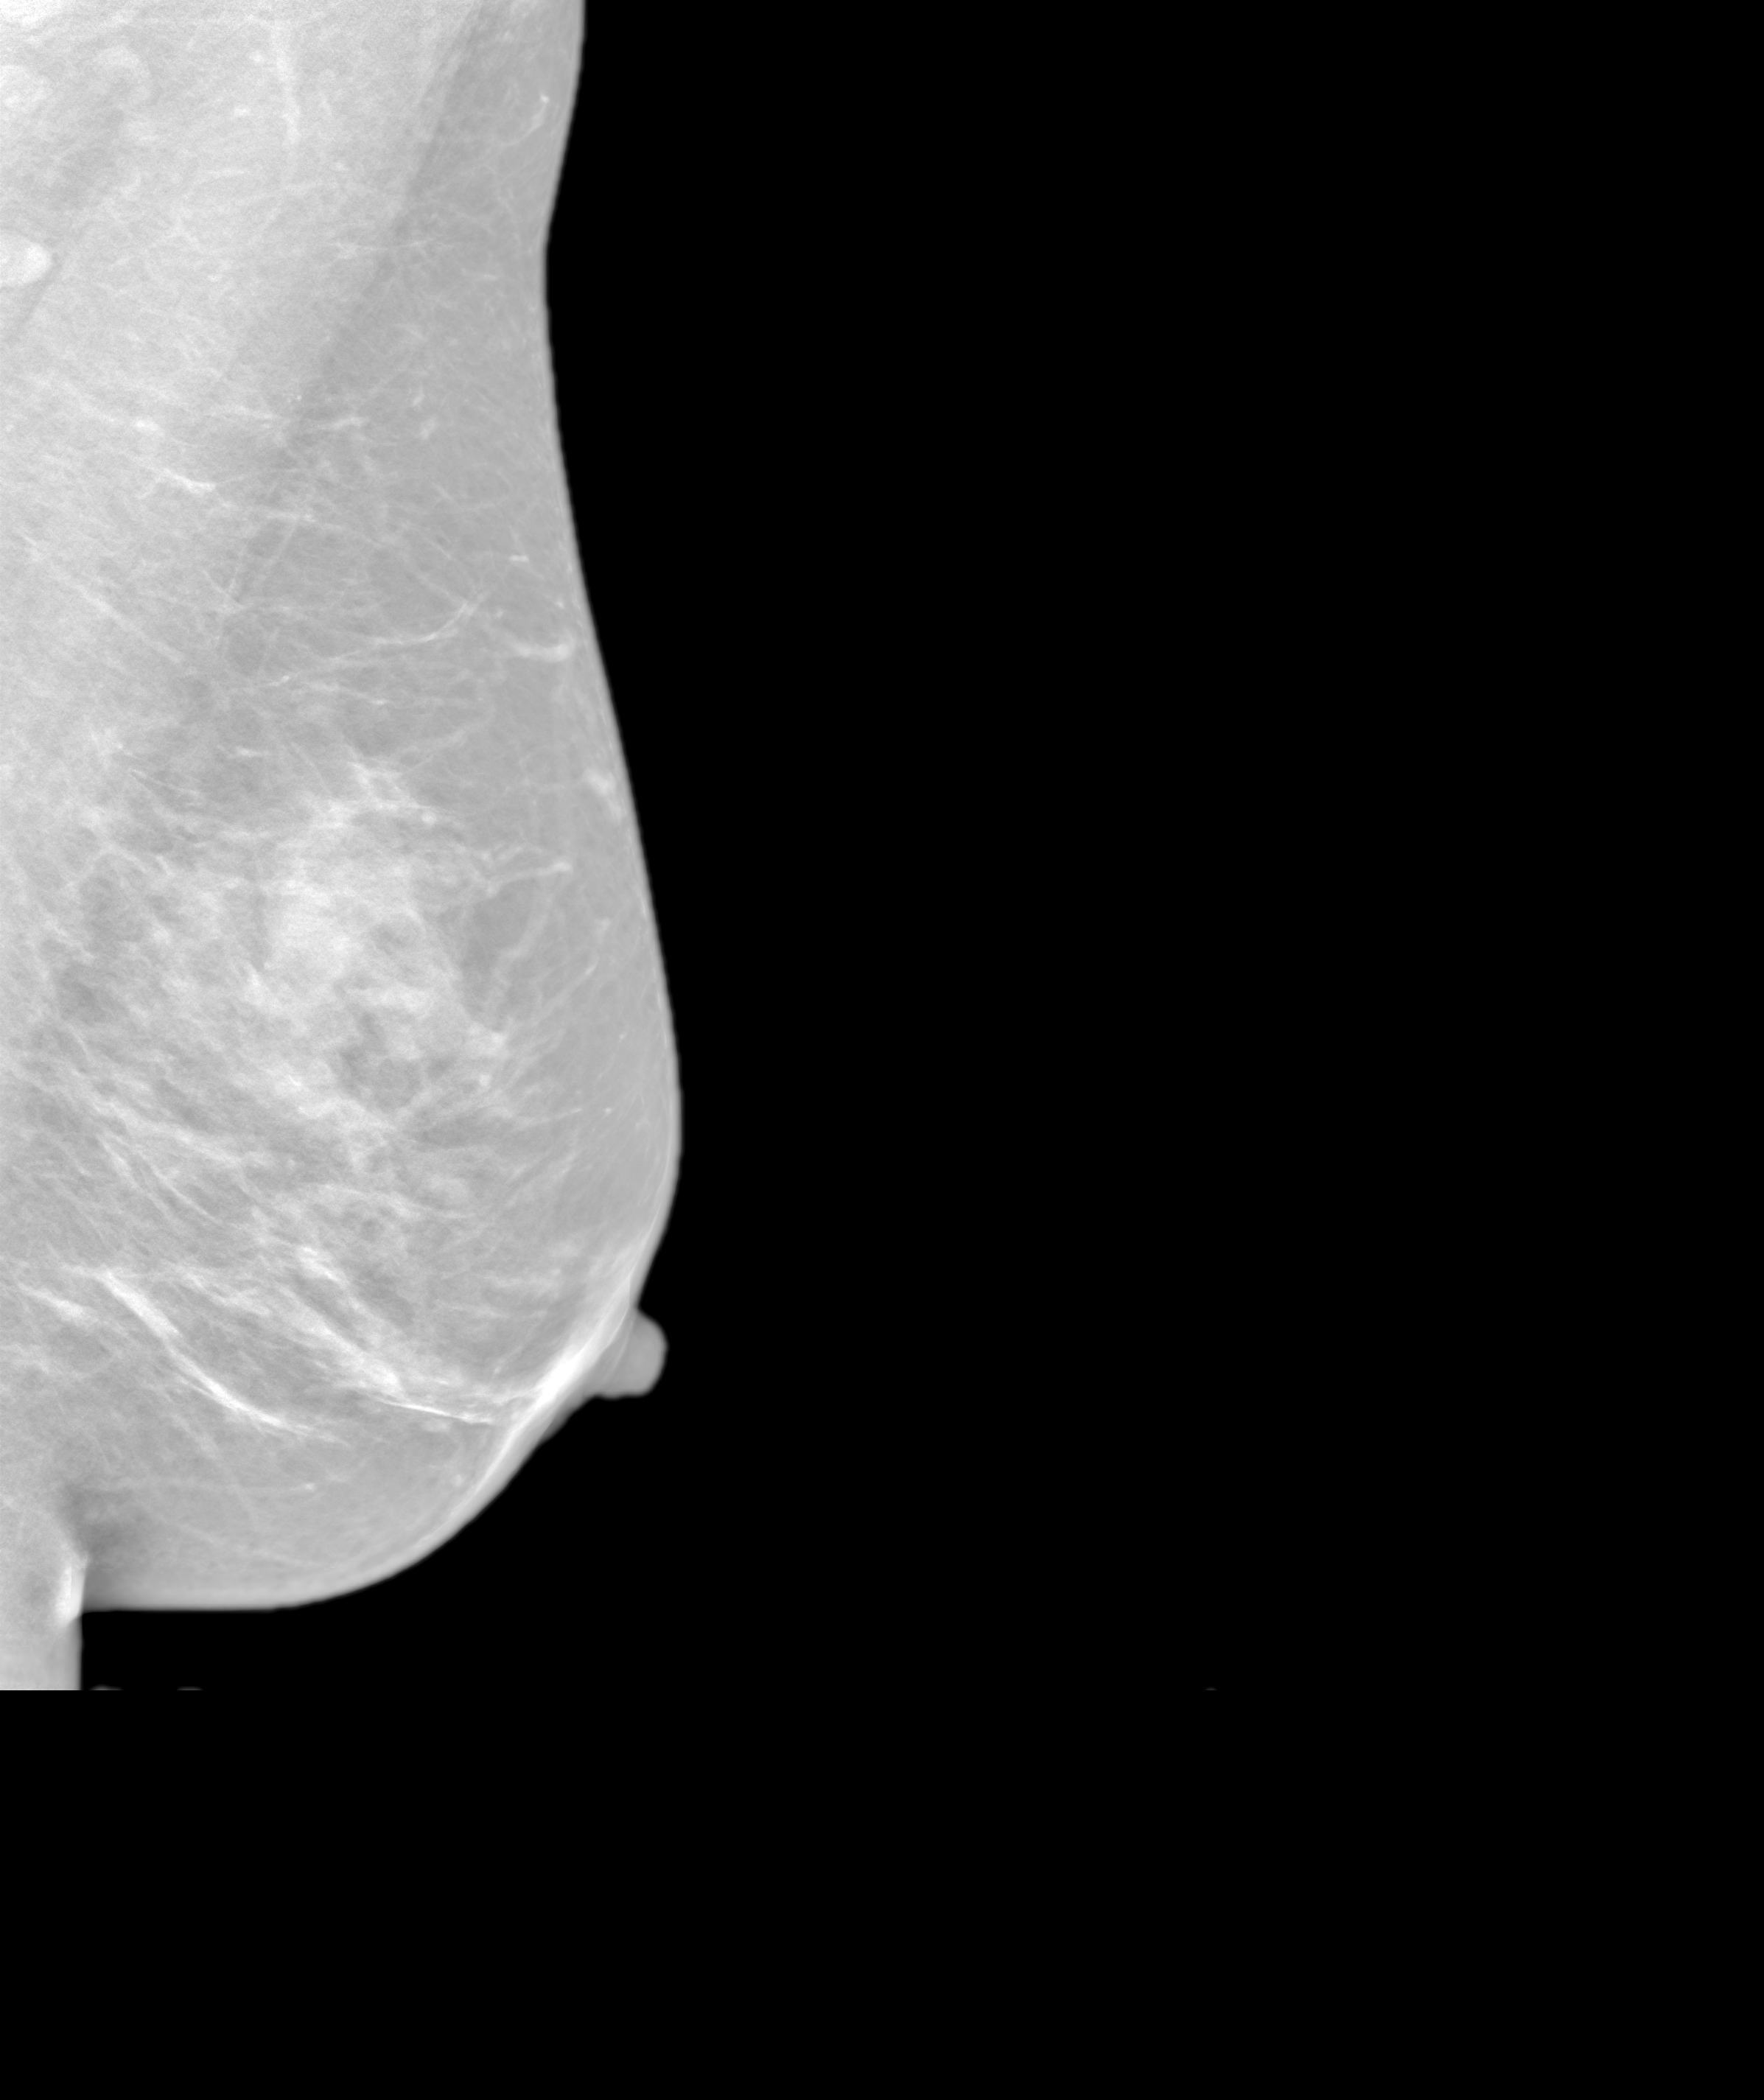
Synthetic 2-D view generated from a tomosynthesis acquisition (not an FFDM exposure); left breast; MLO view; screening examination; system: SenoIris_1SP1.1(421). Patient aged 48 years (female).
- breast density at the screening exam (both breasts): heterogeneously dense (BI-RADS density category c)
- final BI-RADS assessment for this screening round (tomosynthesis exam, both breasts): category 1
- recall: no recall after this screen